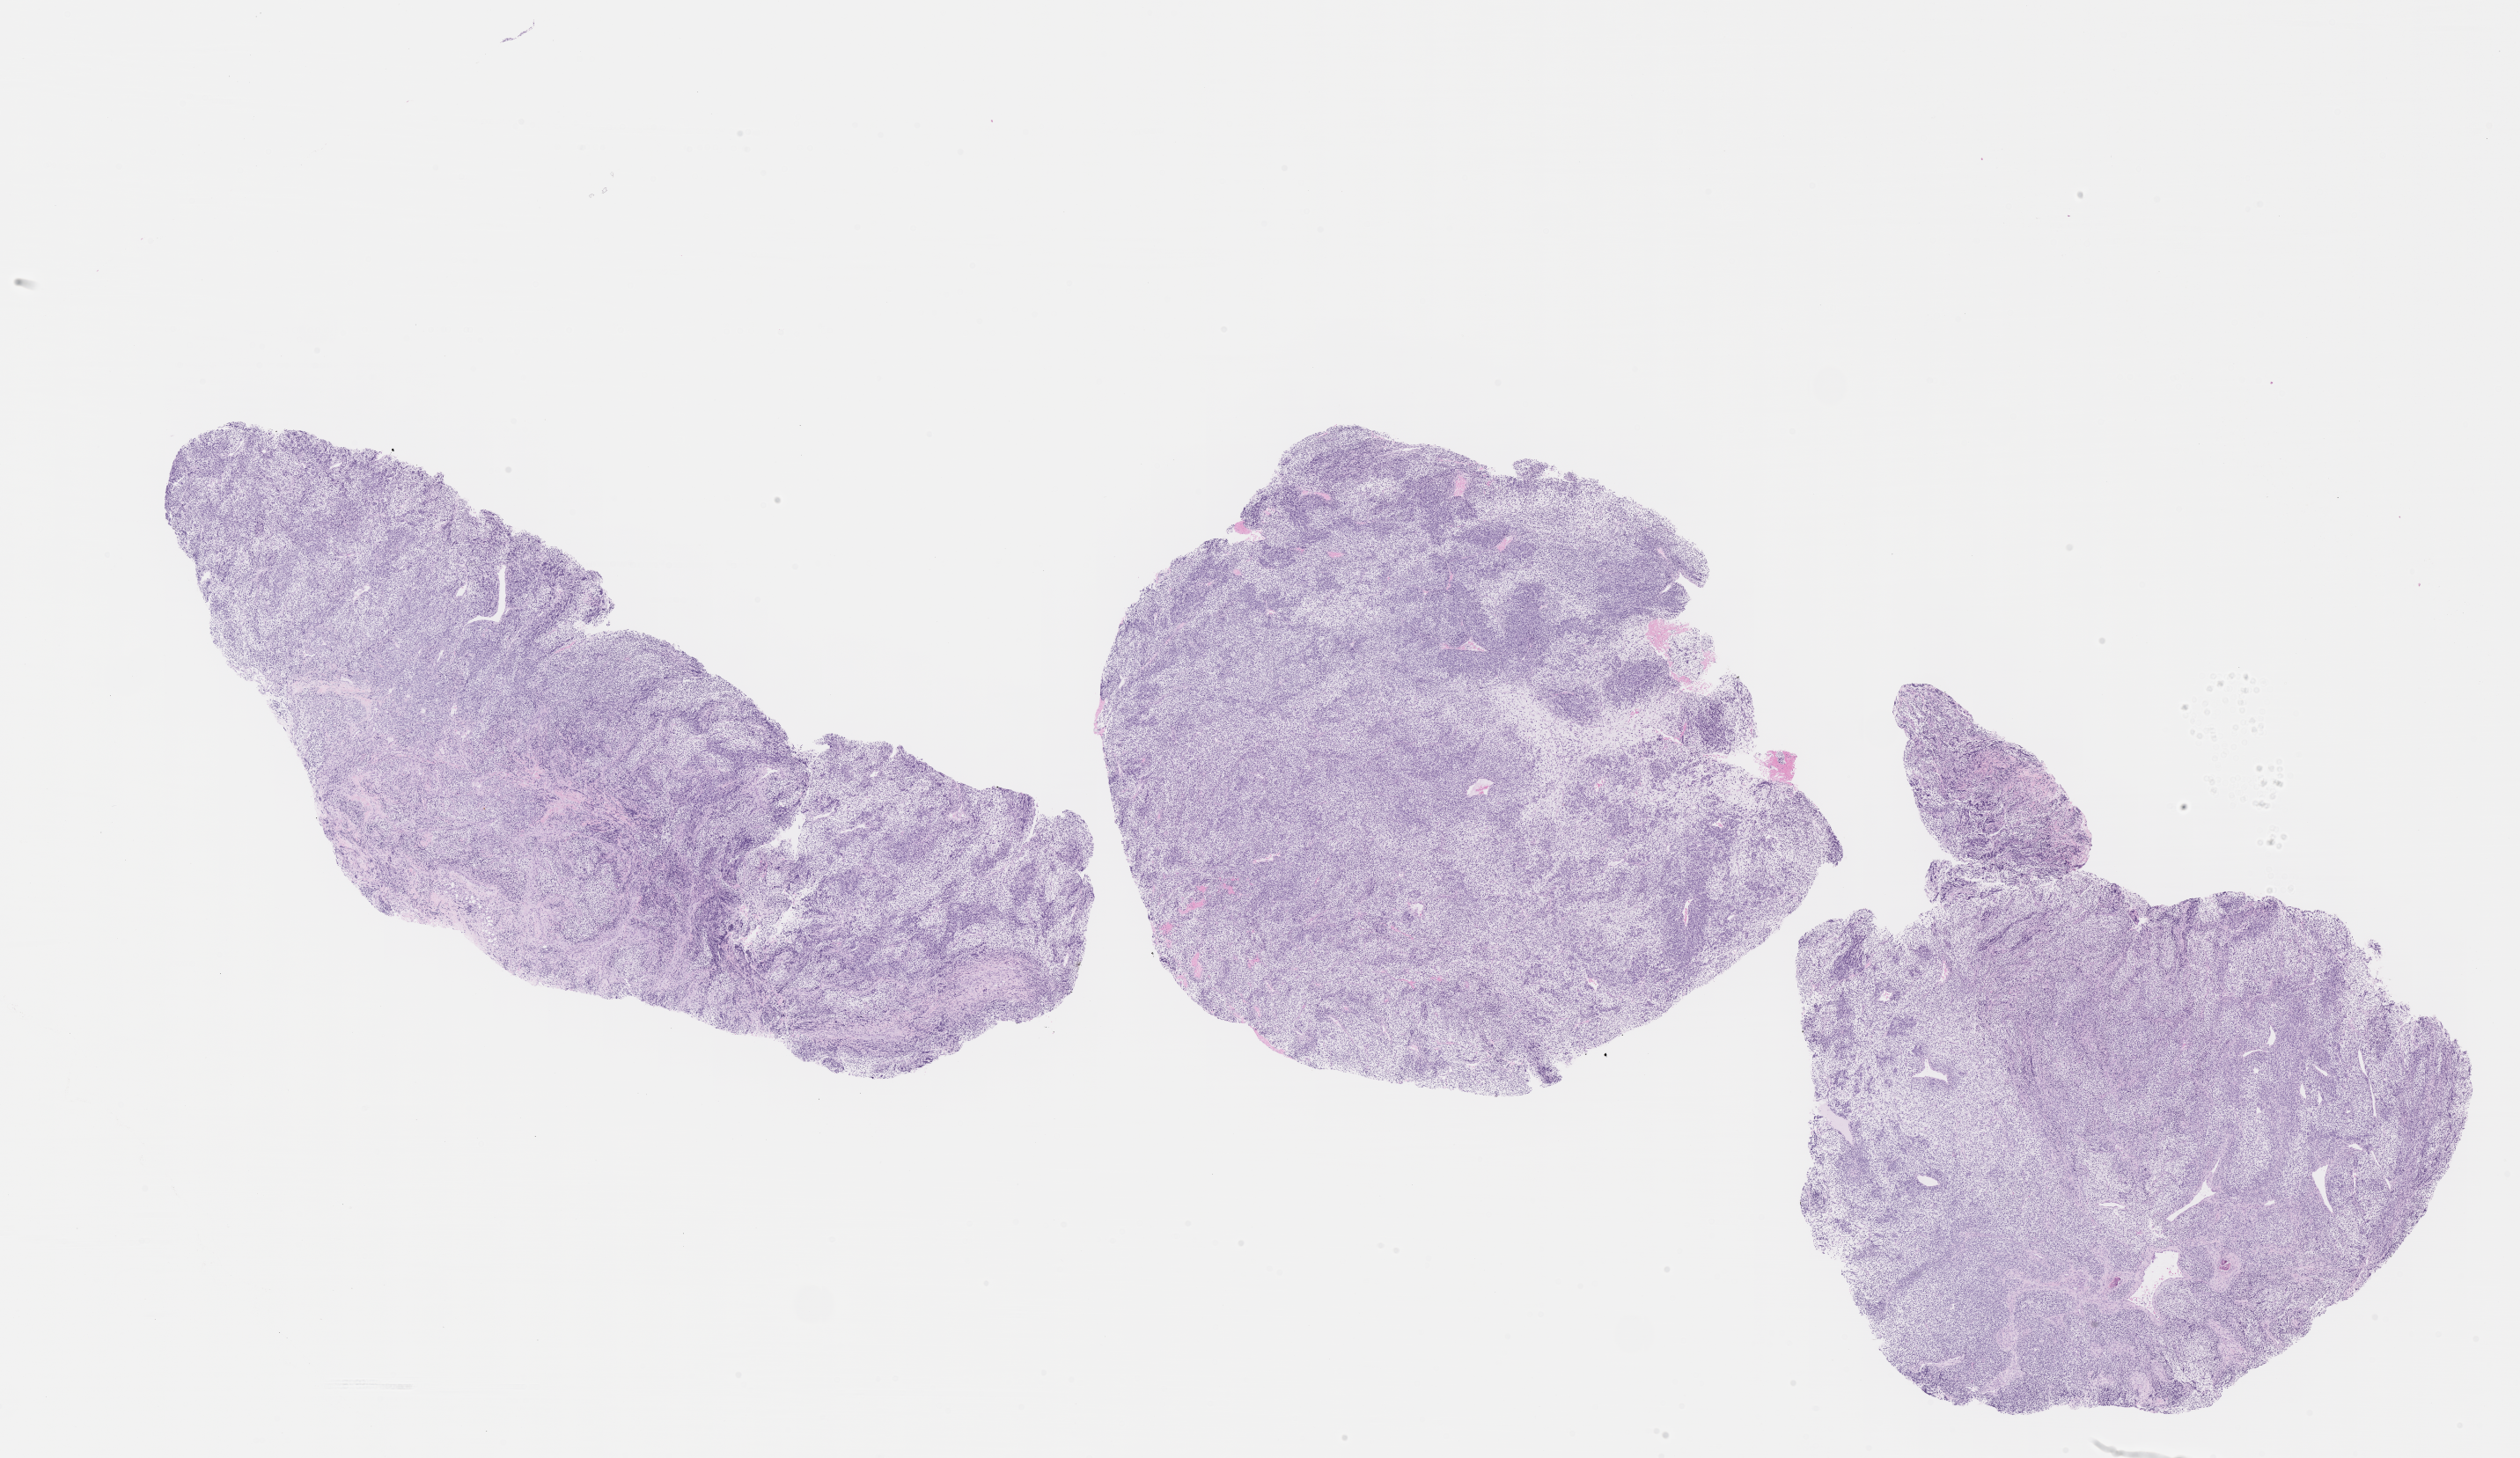
Whole-slide image, hematoxylin and eosin (H&E) stain of tumor tissue, whole scanned area (about 23.1 x 13.4 mm) shown as a low-resolution overview; FFPE section; site: soft tissue, ear-left. Male patient, age at diagnosis 4.9 years.
Metastatic status at presentation (as recorded): non-metastatic. Diagnosis: rhabdomyosarcoma; histological classification: embryonal rhabdomyosarcoma. Stage (as recorded): 2.